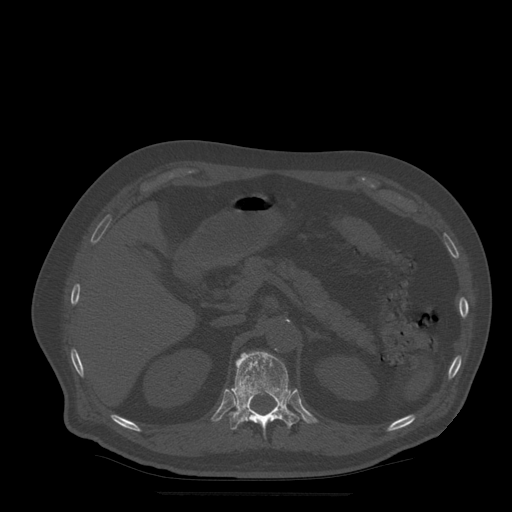
CT including the spine, one axial slice; position 220 of 522 along the scan axis; bone window (W 1800 / L 400 HU); 512 × 512 image matrix. Patient age 72 years. From the clinical record (not read from this slice): primary cancer: prostate.
Annotated regions visible in this slice (semi-automatically segmented with operator editing):
- T12 vertebra: bounding box <229,352,300,432> (left, top, right, bottom; pixels)